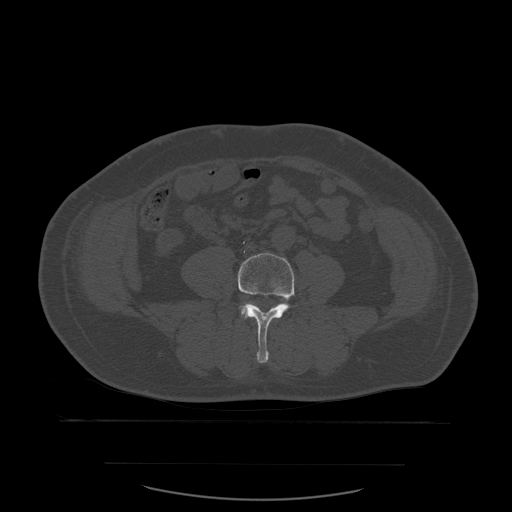
CT including the spine, one axial slice; slice 162 of 590 in the series (ordered by position); bone window (W 1800 / L 400 HU); 512 × 512 image matrix, field of view 479 × 479 mm. Patient age 71 years. Case-level facts recorded for this patient, not image findings: primary cancer: lung; vertebrae with lytic lesions (as recorded): T1, T2, L5, S1.
Outlined on this slice (semi-automatic segmentation, software-assisted and operator-edited):
- L4 vertebra: bounding box (x1, y1, x2, y2) in pixels: (238, 253, 295, 363)
- L5 vertebra: (244, 302, 254, 306)